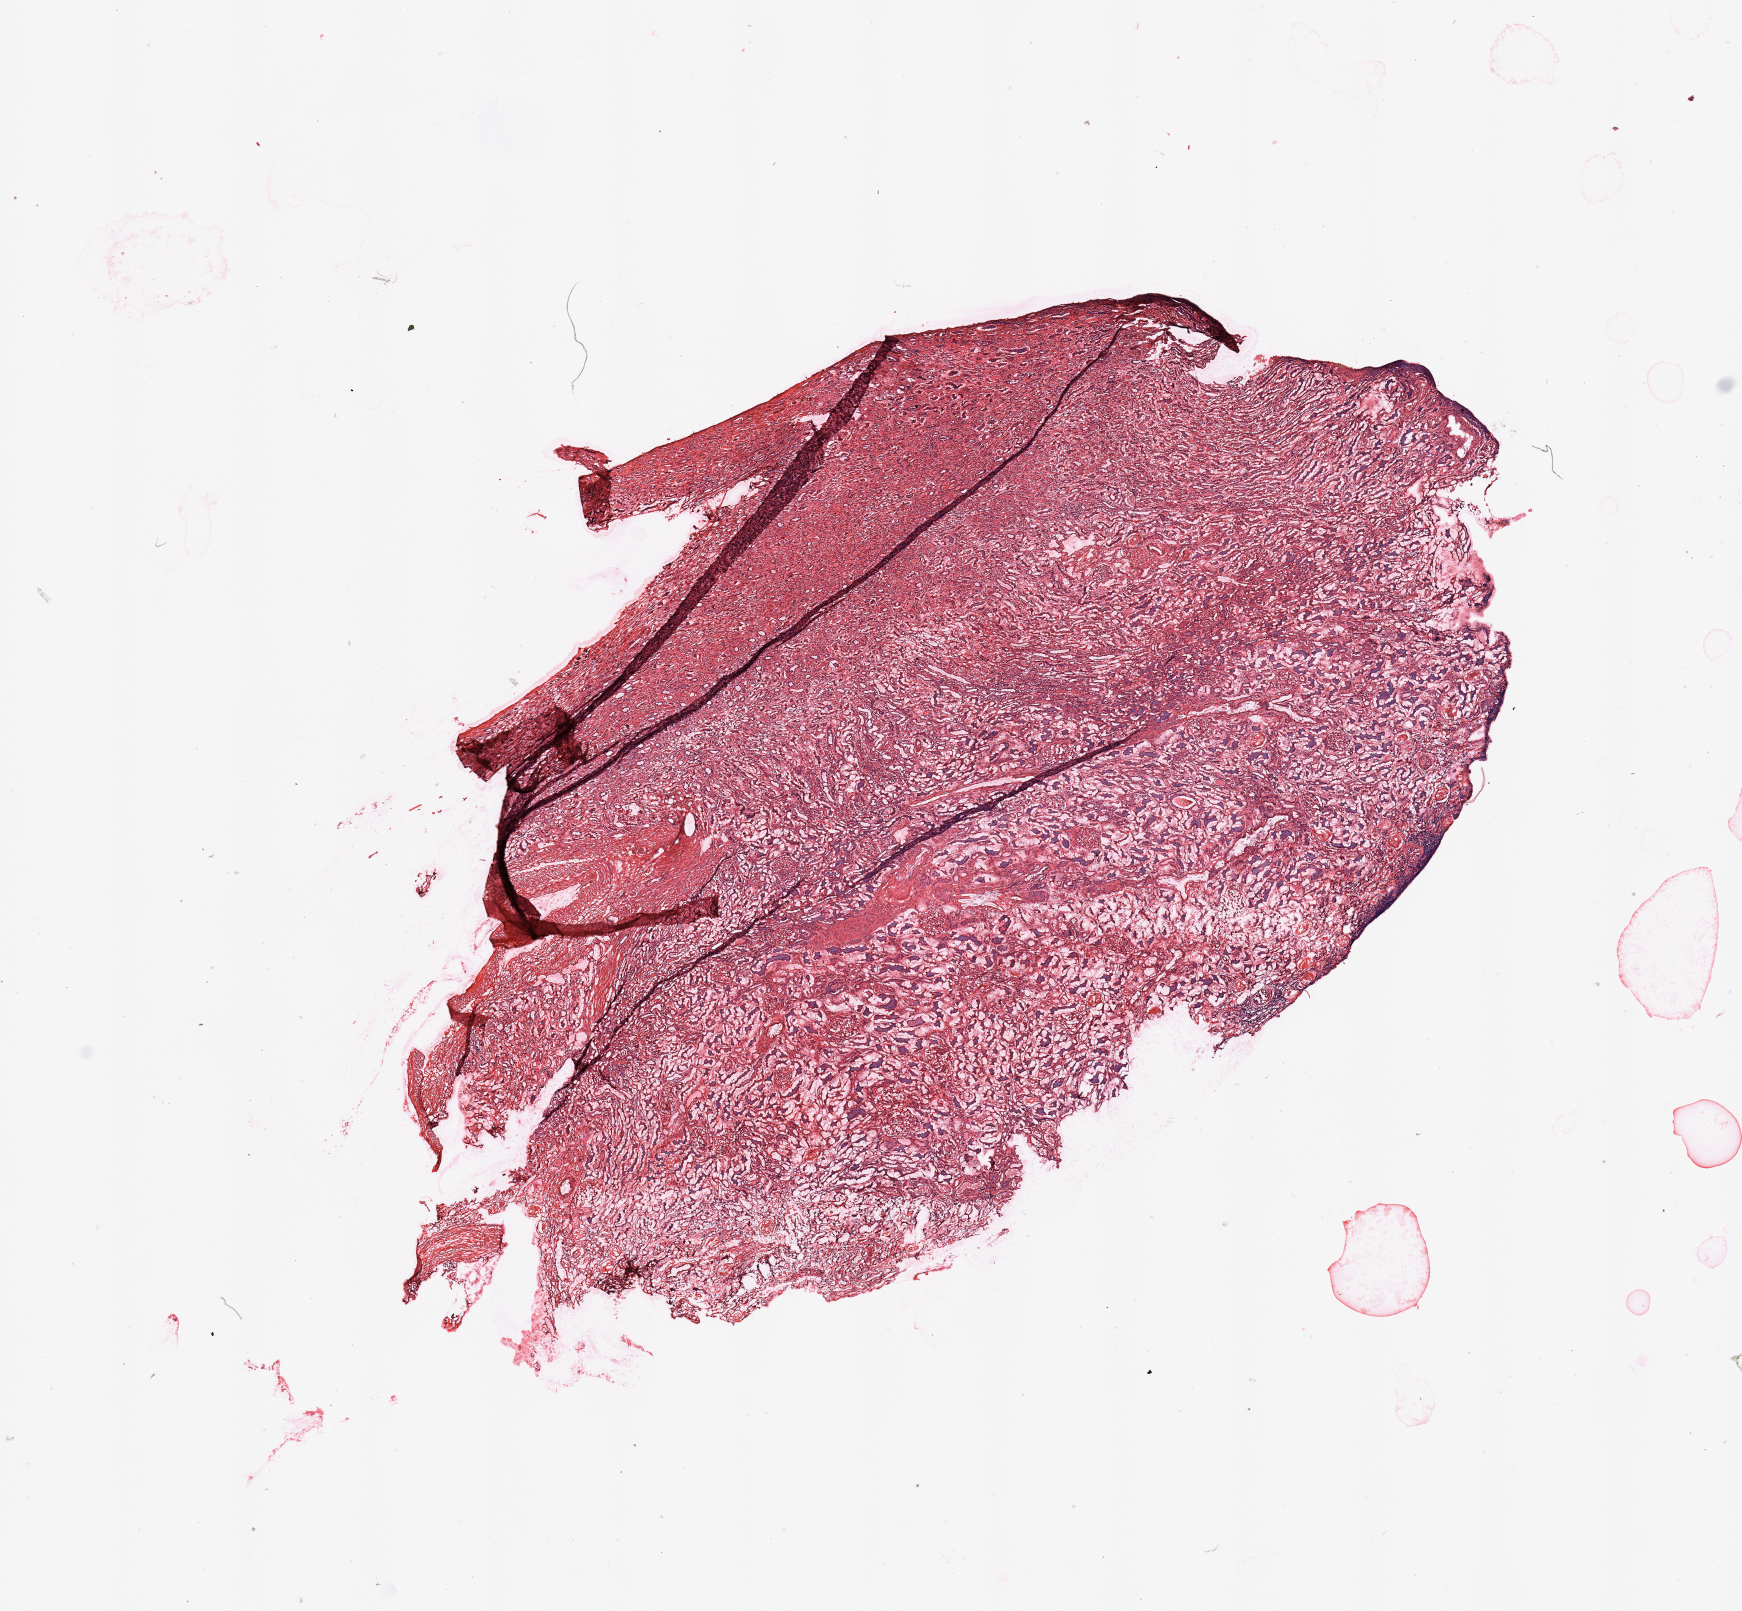
H&E-stained whole-slide image, shown as a low-resolution overview of the whole scanned area (about 13.8 x 12.7 mm, from a 20x scan); normal (non-tumour) tissue sample, sampled site: kidney. 62-year-old male patient.
This section: normal (non-tumour) tissue from the same patient. Patient diagnosis: Renal cell carcinoma, NOS.